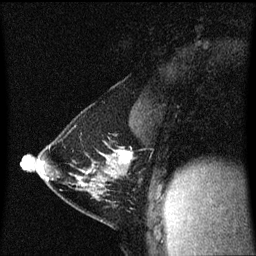
Breast MRI (dynamic contrast-enhanced), one sagittal slice; position 34 of 60 along the scan axis; dynamic contrast-enhanced series, image 2 of 3 at this slice position (ordered by acquisition); 1.5 T; TE 4.2 ms, TR 8.4 ms; 2 mm slice thickness; 256 × 256 image matrix, field of view 200 × 200 mm. Patient: female, 40 years. From the clinical record (not read from this slice): setting: breast cancer imaged before/during neoadjuvant chemotherapy; receptor status: triple-negative.
Outlined on this slice (semi-automatically segmented with operator editing):
- analysis volume of interest (the breast-tissue region the enhancement analysis was run in; not a lesion): box from (x=34, y=142) to (x=134, y=199) px
- tumour enhancement mask (voxels above the 70 % enhancement threshold inside the analysis volume of interest): (x=120, y=152)–(x=132, y=163)